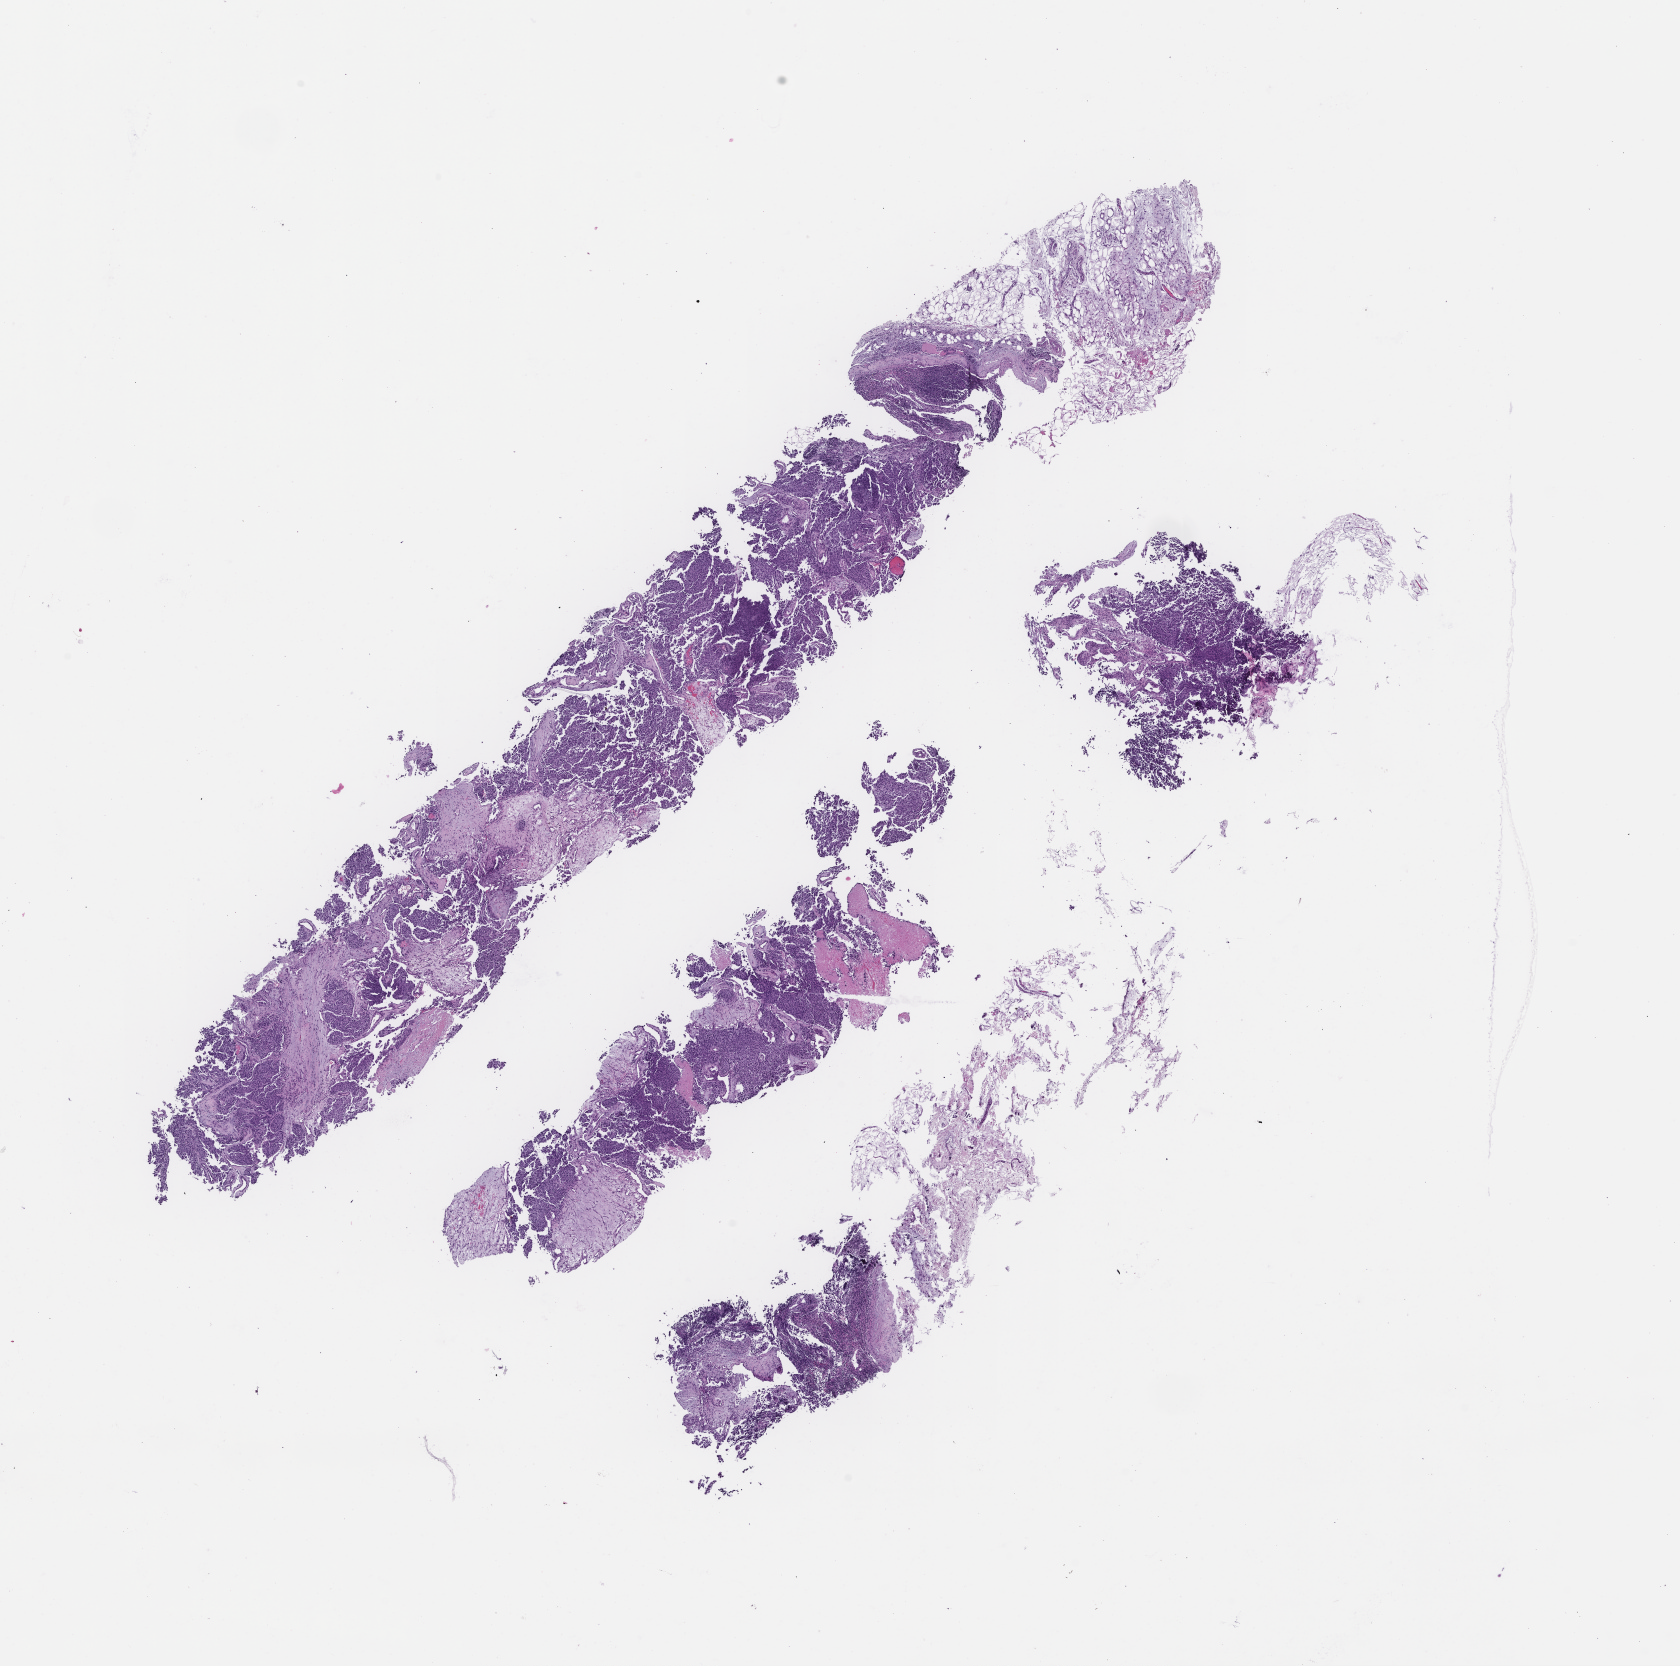
Digitized H&E-stained section, a low-resolution overview of the entire scanned area, about 13.6 x 13.5 mm; formalin-fixed, paraffin-embedded (FFPE) tissue; archival tissue. Female patient.
This section: metastasis (sampled organ not recorded). Patient diagnosis (primary): Invasive Breast Carcinoma.